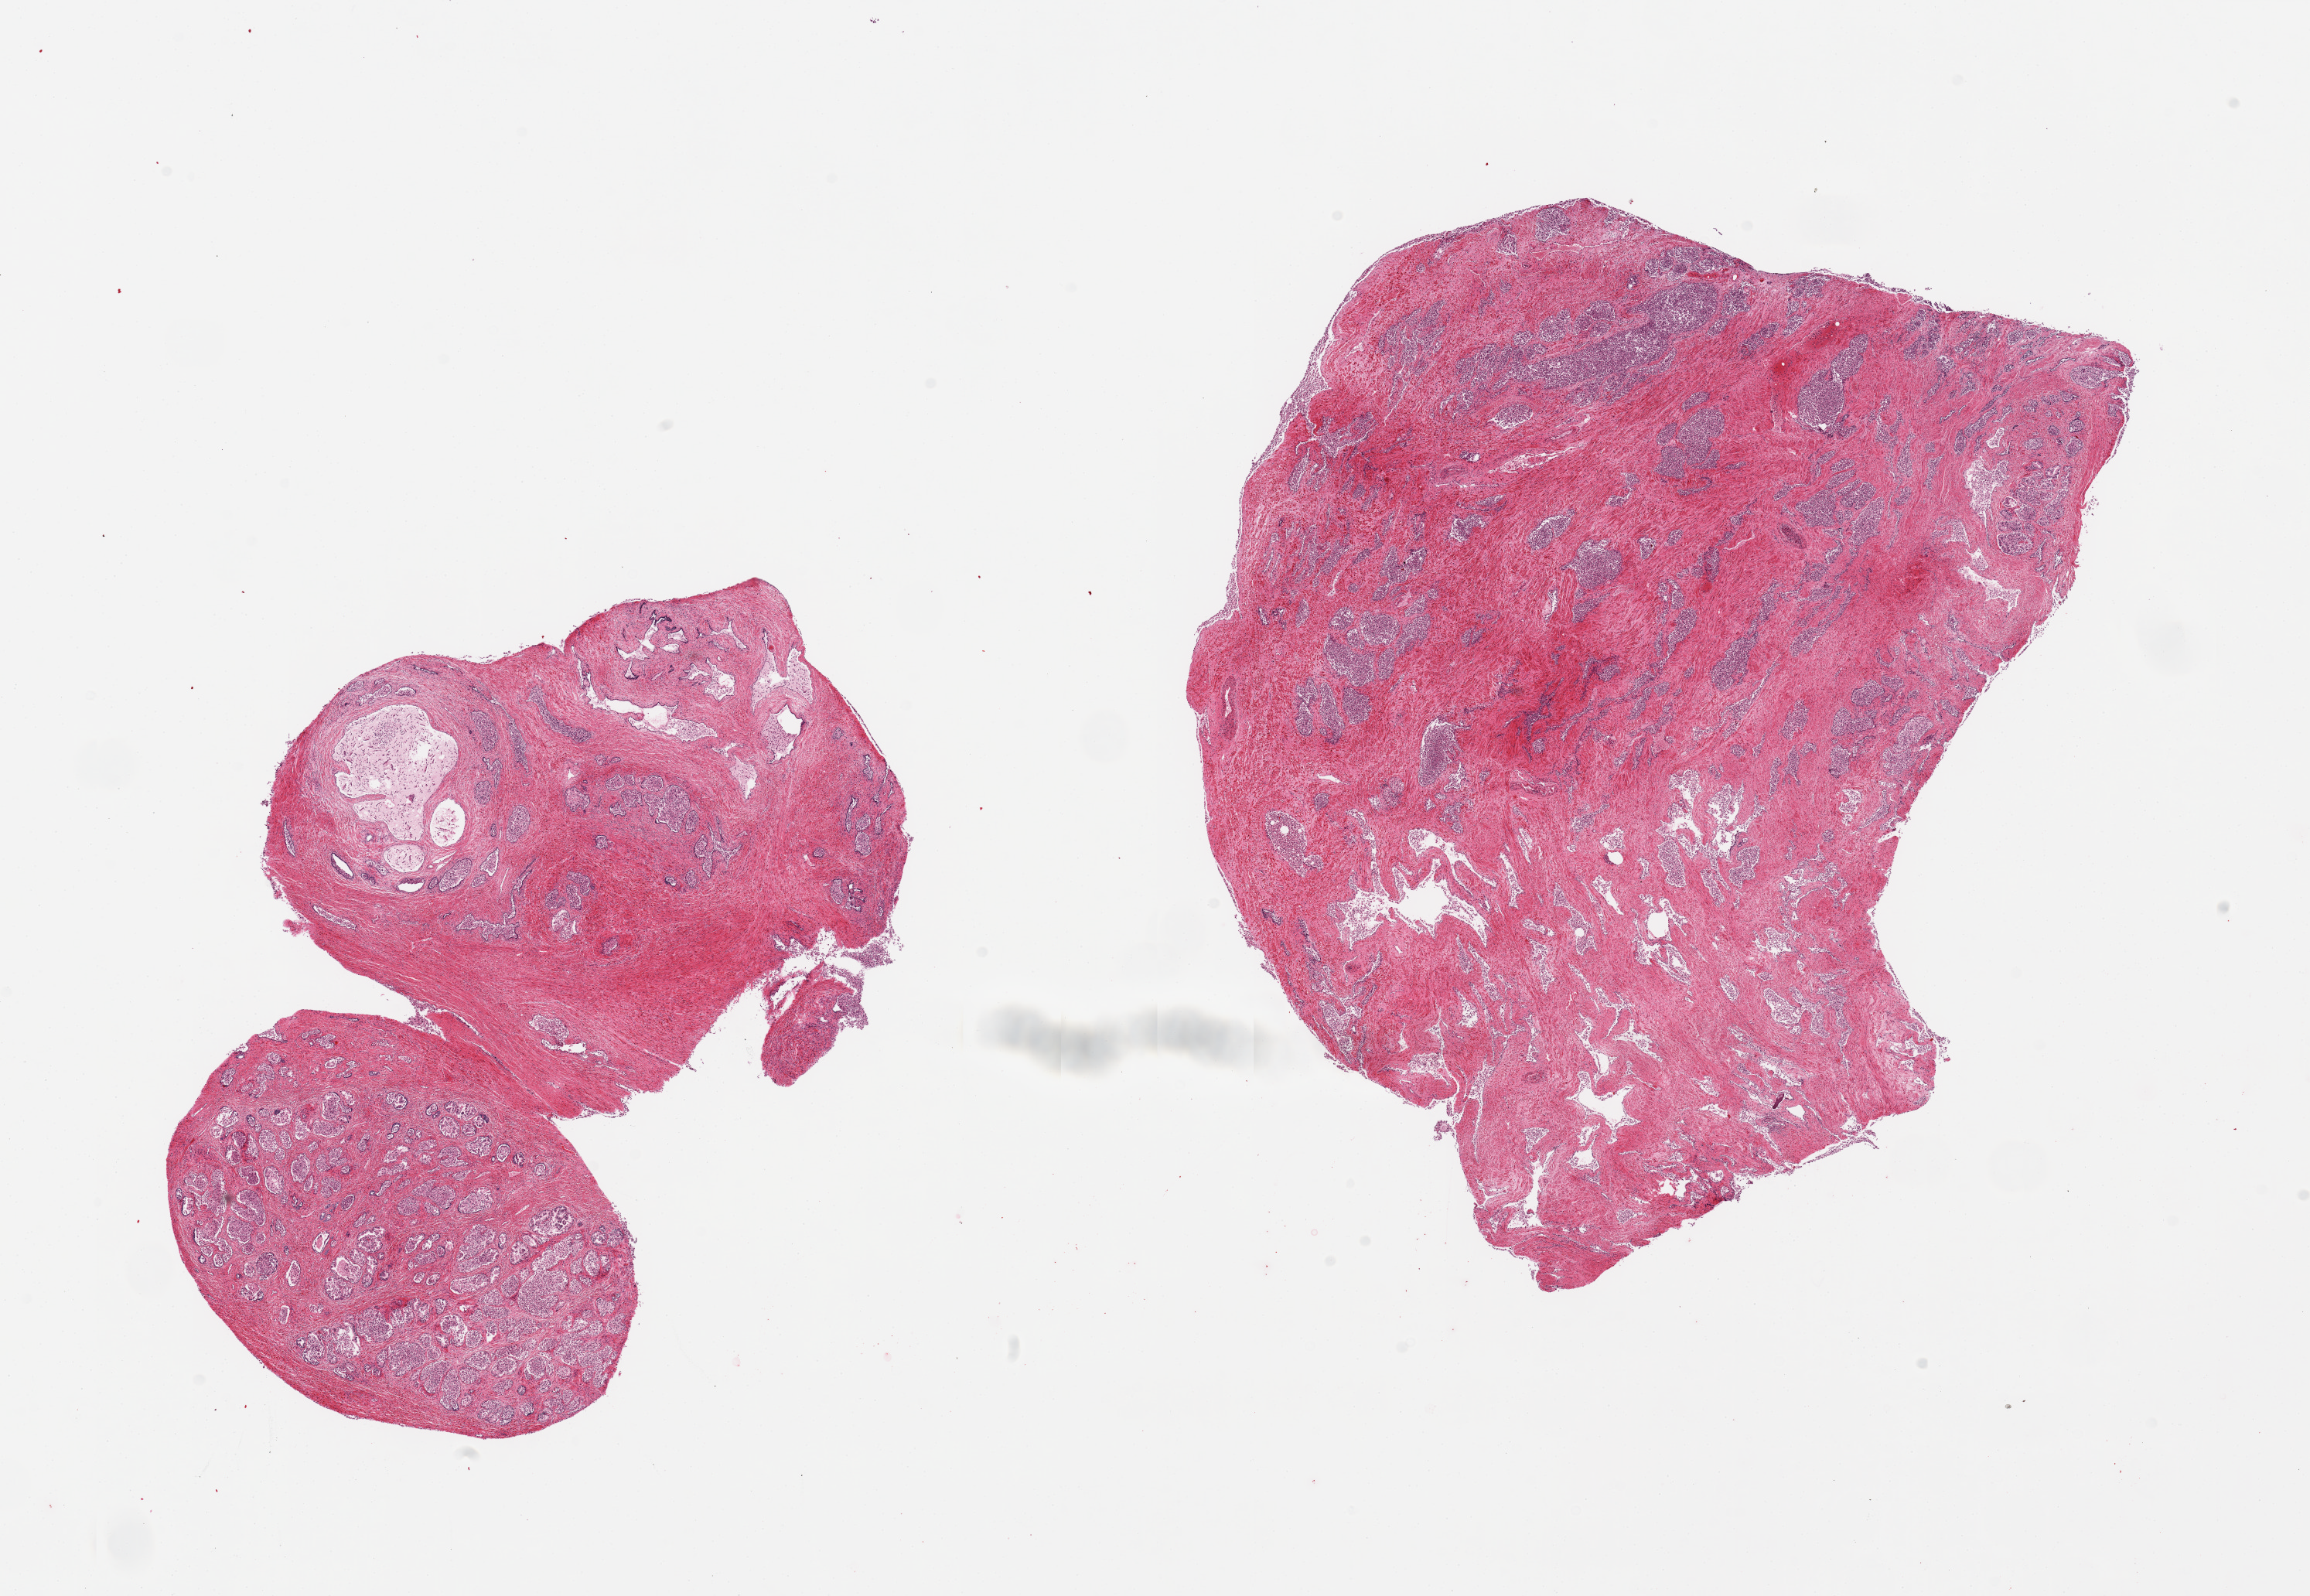
Haematoxylin and eosin whole-slide image, brightfield, low-resolution overview of the scanned area, about 23.6 x 16.3 mm (slide scanned at 20x); PAXgene-fixed paraffin-embedded (PFPE) section; target tissue: prostate; donor tissue sample. Donor sex: male.
Reviewer comment on this tissue sample: 2 pieces, severe glandular autolysis.